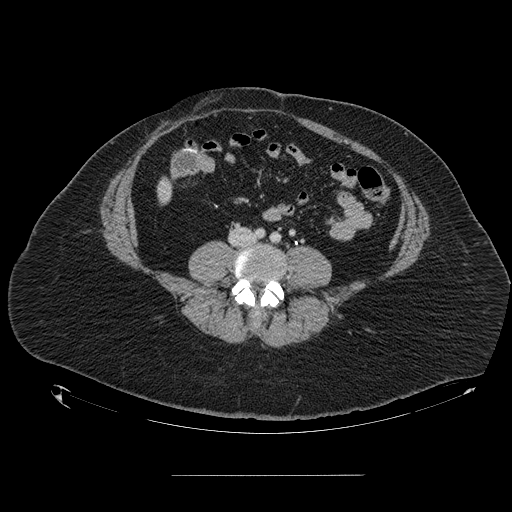
Contrast-enhanced abdominal CT, one axial slice; position 8 of 164 along the scan axis; intravenous contrast given; soft-tissue window (W 400 / L 40 HU); 2.5 mm slice thickness; 512 × 512 image matrix. Female patient, age 52 years. From the clinical record (not read from this slice): diagnosis: colorectal cancer liver metastases, imaged before liver resection; multiple liver metastases: yes.
Outlined on this slice (manually delineated by an expert):
- liver: box from (x=158, y=181) to (x=172, y=200) px